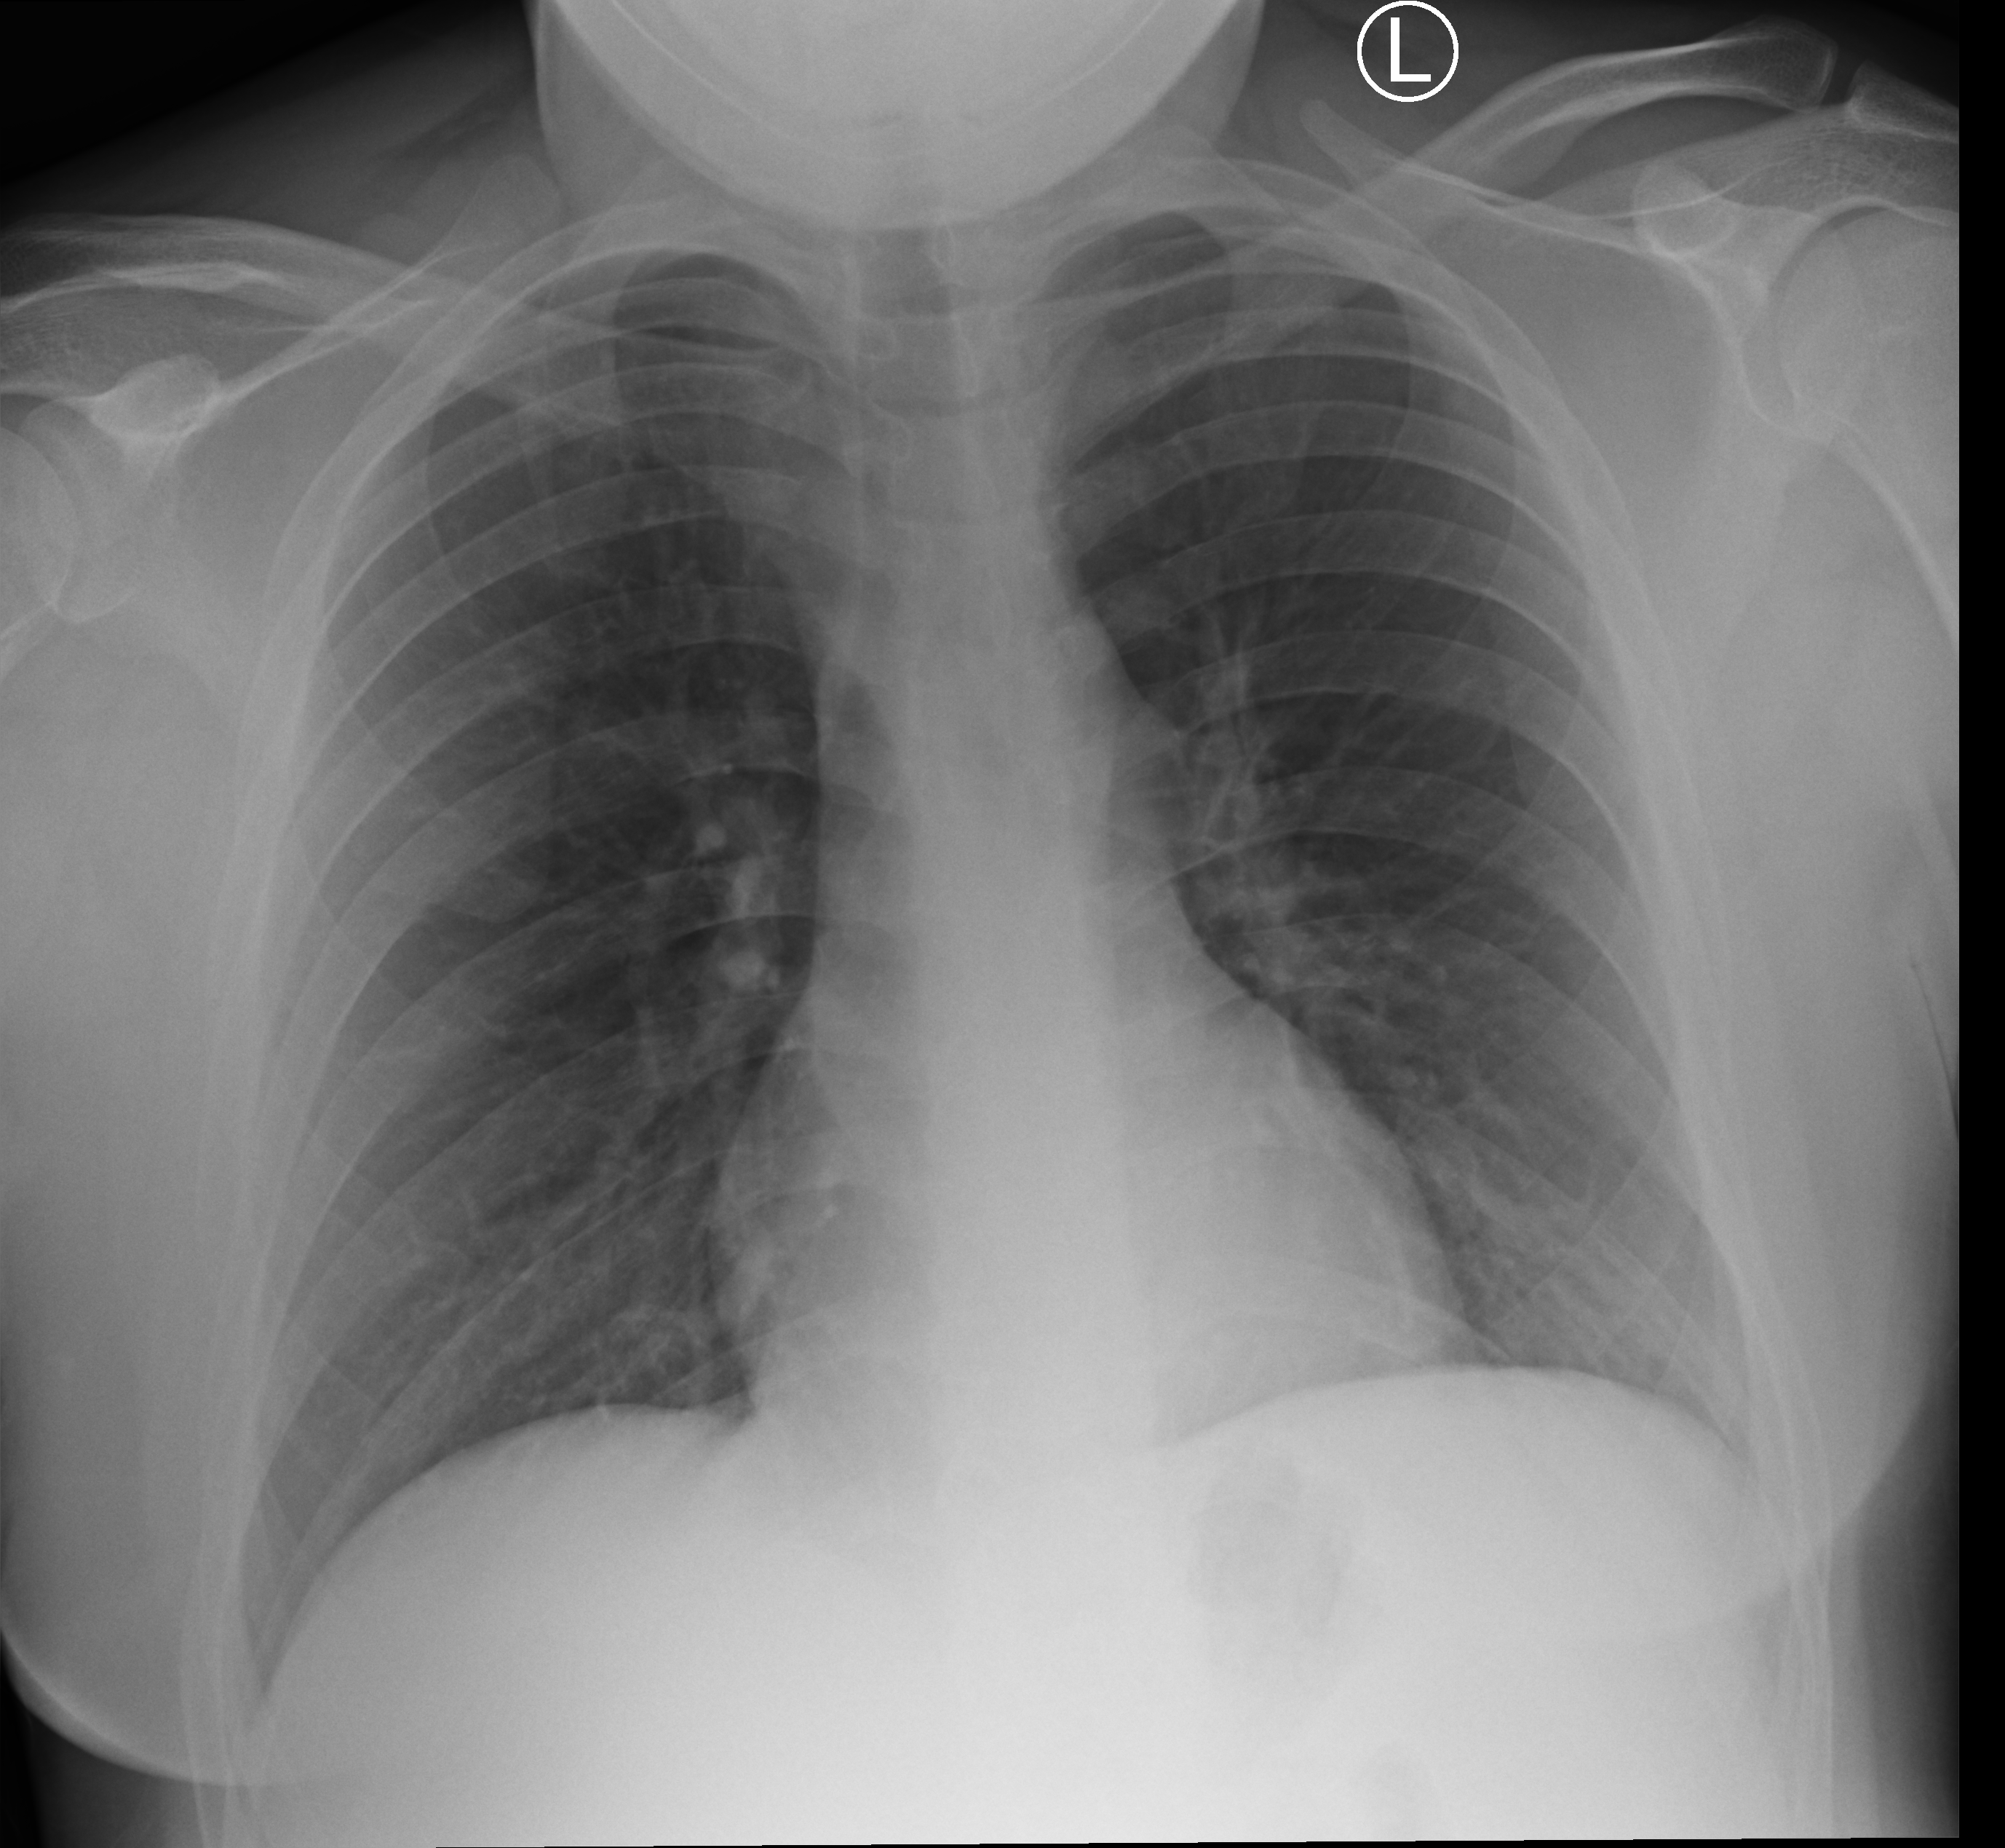
Bedside chest radiograph (computed radiography); anteroposterior (AP) projection. Male patient hospitalised with COVID-19, age 18–59 years.
From the hospital-stay record, not from the radiograph (when in the stay this image was taken is not recorded):
- diabetes (admission record): no
- COPD (admission record): no
- mechanically ventilated during this hospital stay: no